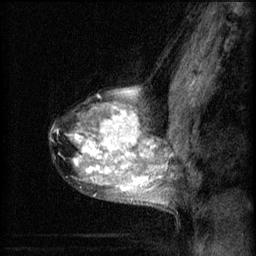
Breast MRI (dynamic contrast-enhanced), one sagittal slice; slice 44 of 60 in the series (ordered by position); 3 images stored at this slice position (order not interpretable as contrast timing); 1.5 T; TE 4.2 ms, TR 8.2 ms; 2 mm slice thickness; 256 × 256 image matrix, field of view 180 × 180 mm. Patient: female, 40 years.
Outlined on this slice (semi-automatic segmentation, software-assisted and operator-edited):
- analysis volume of interest (the breast-tissue region the enhancement analysis was run in; not a lesion): box from (x=52, y=80) to (x=167, y=209) px
- tumour enhancement mask (voxels above the 70 % enhancement threshold inside the analysis volume of interest): (x=73, y=88)–(x=167, y=203)